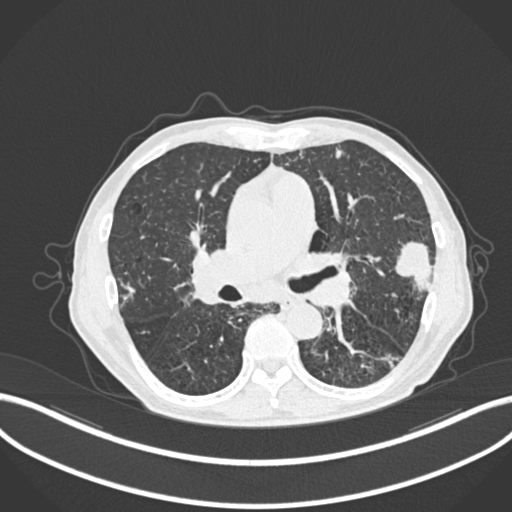
Chest CT, one axial slice. Position 132 of 287 along the scan axis. Reconstruction kernel B30f. Lung window (W 1500 / L -600 HU). 1 mm slice thickness. 512 × 512 image matrix, field of view 400 × 400 mm. Patient: male, 74 years. From the clinical record (not read from this slice): clinical TNM (as recorded): T2a N1 M0.
Structures marked on this image (rectangle marked by the reading radiologist):
- lung tumour (recorded histology: adenocarcinoma): bounding box <395,238,433,296> (left, top, right, bottom; pixels)